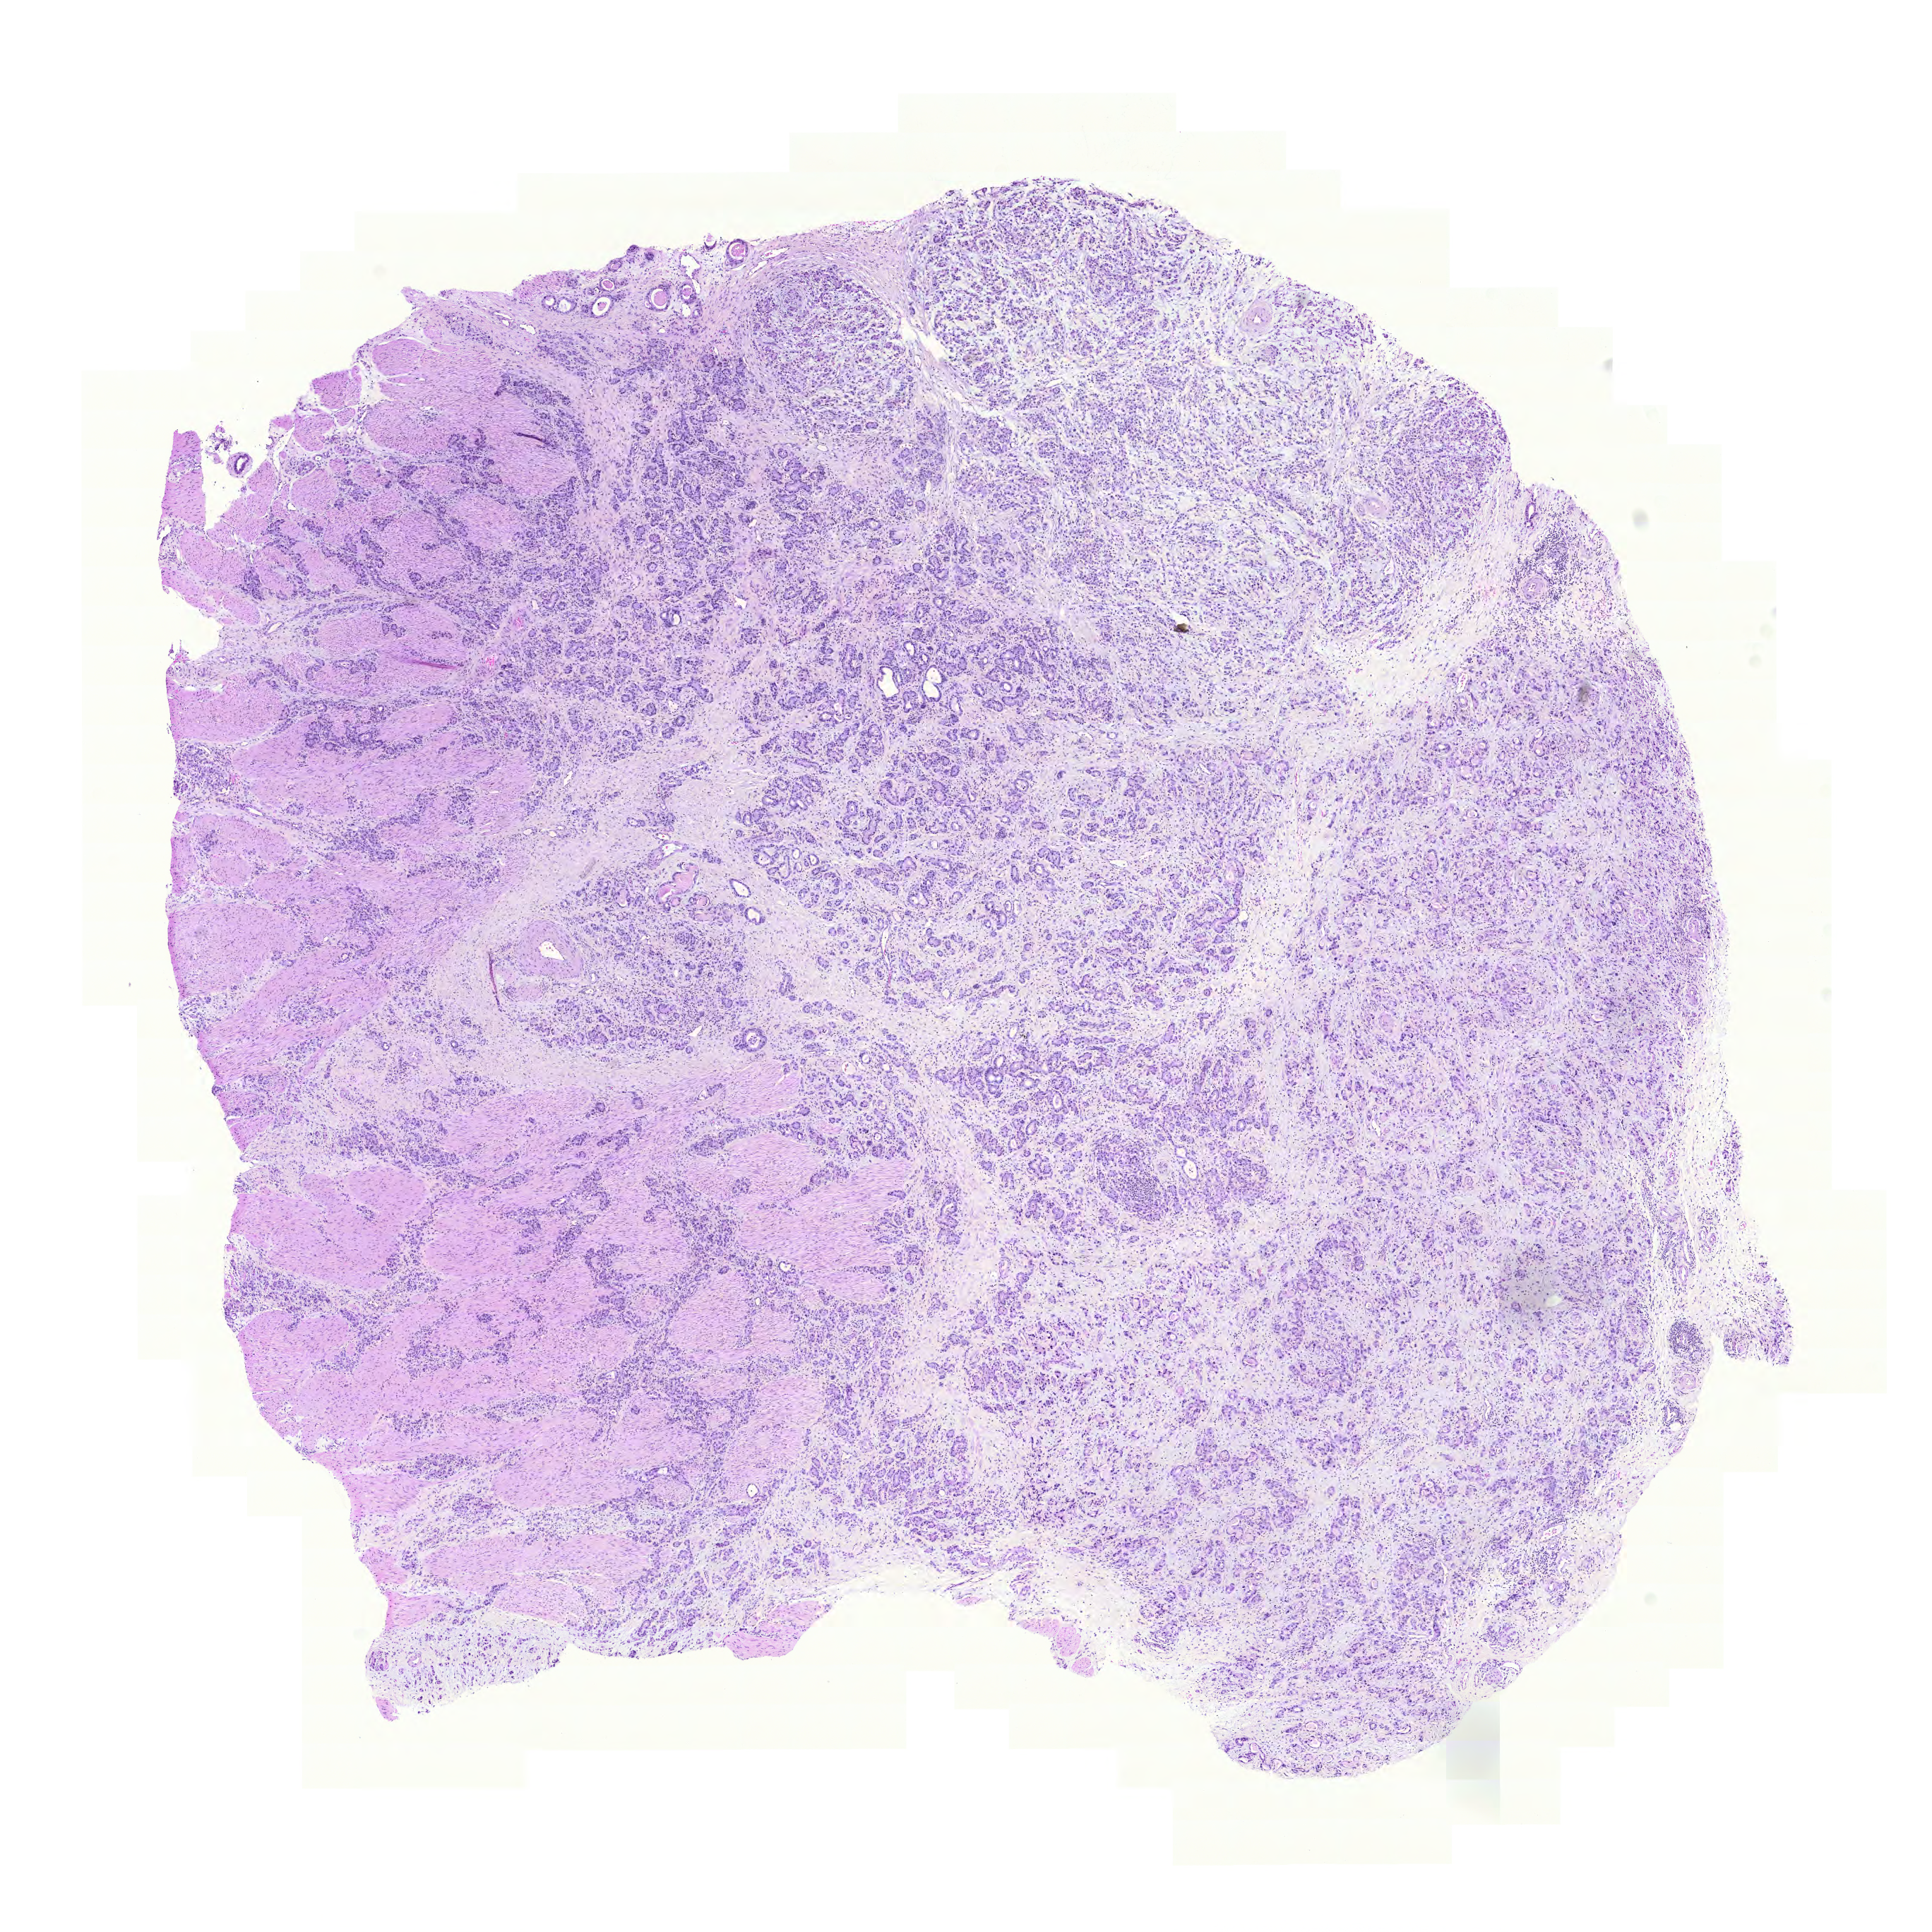
H&E whole-slide image, whole scanned area (about 10.2 x 10.2 mm, slide scanned at 20x) shown as a low-resolution overview, FFPE section, stomach, primary tumour sample. Male, age 69 years at initial diagnosis. Histologic grade: G3 (poorly differentiated).
Histologic diagnosis: Carcinoma, diffuse type (body of stomach). Lymph nodes positive (case pathology): 12 of 33 examined. AJCC pathologic stage: IIIC (7th edition).